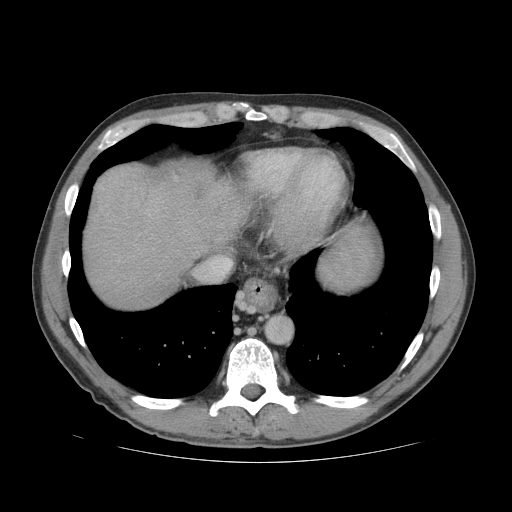
Contrast-enhanced abdominal CT (liver protocol), one axial slice. Slice 68 of 81 in the series (ordered by position). Soft-tissue window (W 400 / L 40 HU). 512 × 512 image matrix, field of view 400 × 400 mm. Case-level facts recorded for this patient, not image findings: diagnosis: hepatocellular carcinoma (patient treated with transarterial chemoembolisation; whether this scan precedes or follows treatment is not stated here); TNM stage (as recorded): Stage-IVB; Child-Pugh class: B; tumour differentiation: well differentiated; tumour nodularity: multinodular.
Structures marked on this image (semi-automatic segmentation, software-assisted and operator-edited):
- liver parenchyma outside the tumour (the mass and vessels are separate outlines, so this box may not span the whole liver): bounding box [x1, y1, x2, y2] px = [82, 162, 244, 308]
- mass: [95, 164, 151, 226]